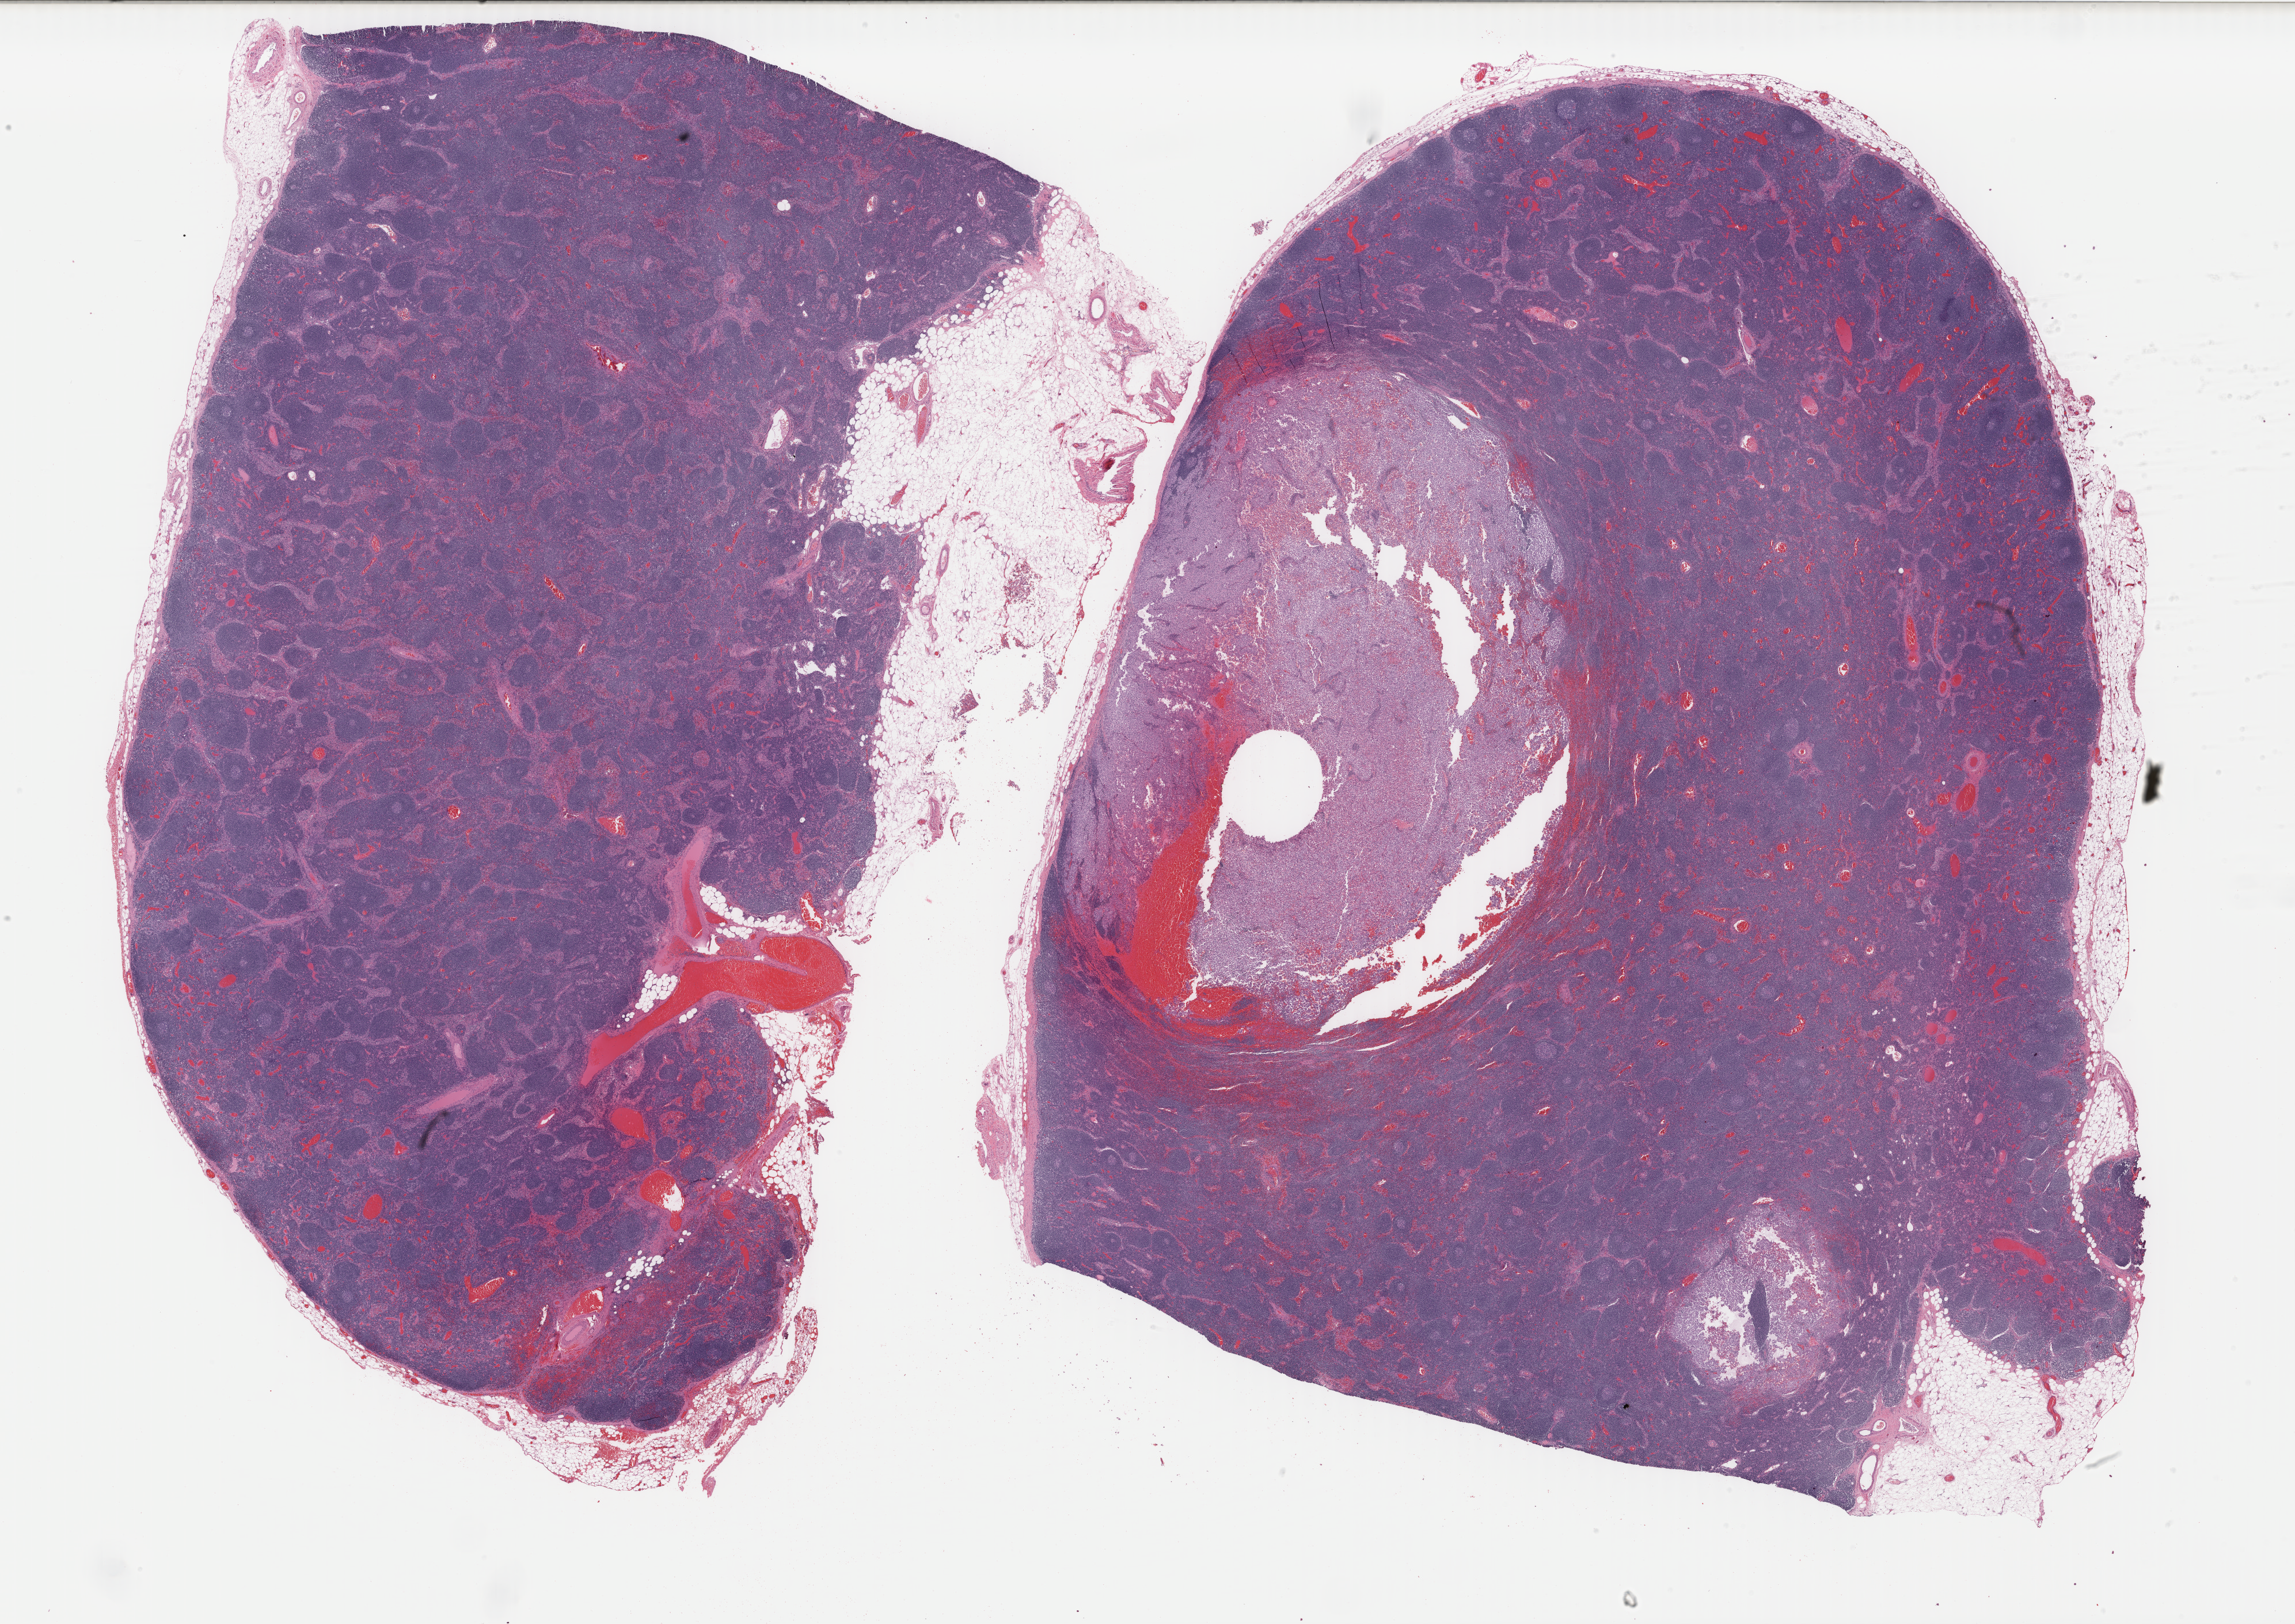
Digitized H&E-stained tissue section (whole slide) — whole scanned area (about 31.6 x 22.4 mm) shown as a low-resolution overview, formalin-fixed paraffin-embedded (FFPE) diagnostic section, skin, primary tumour sample. Patient: male, age at initial diagnosis 36 years.
Histologic diagnosis: Malignant melanoma, NOS.